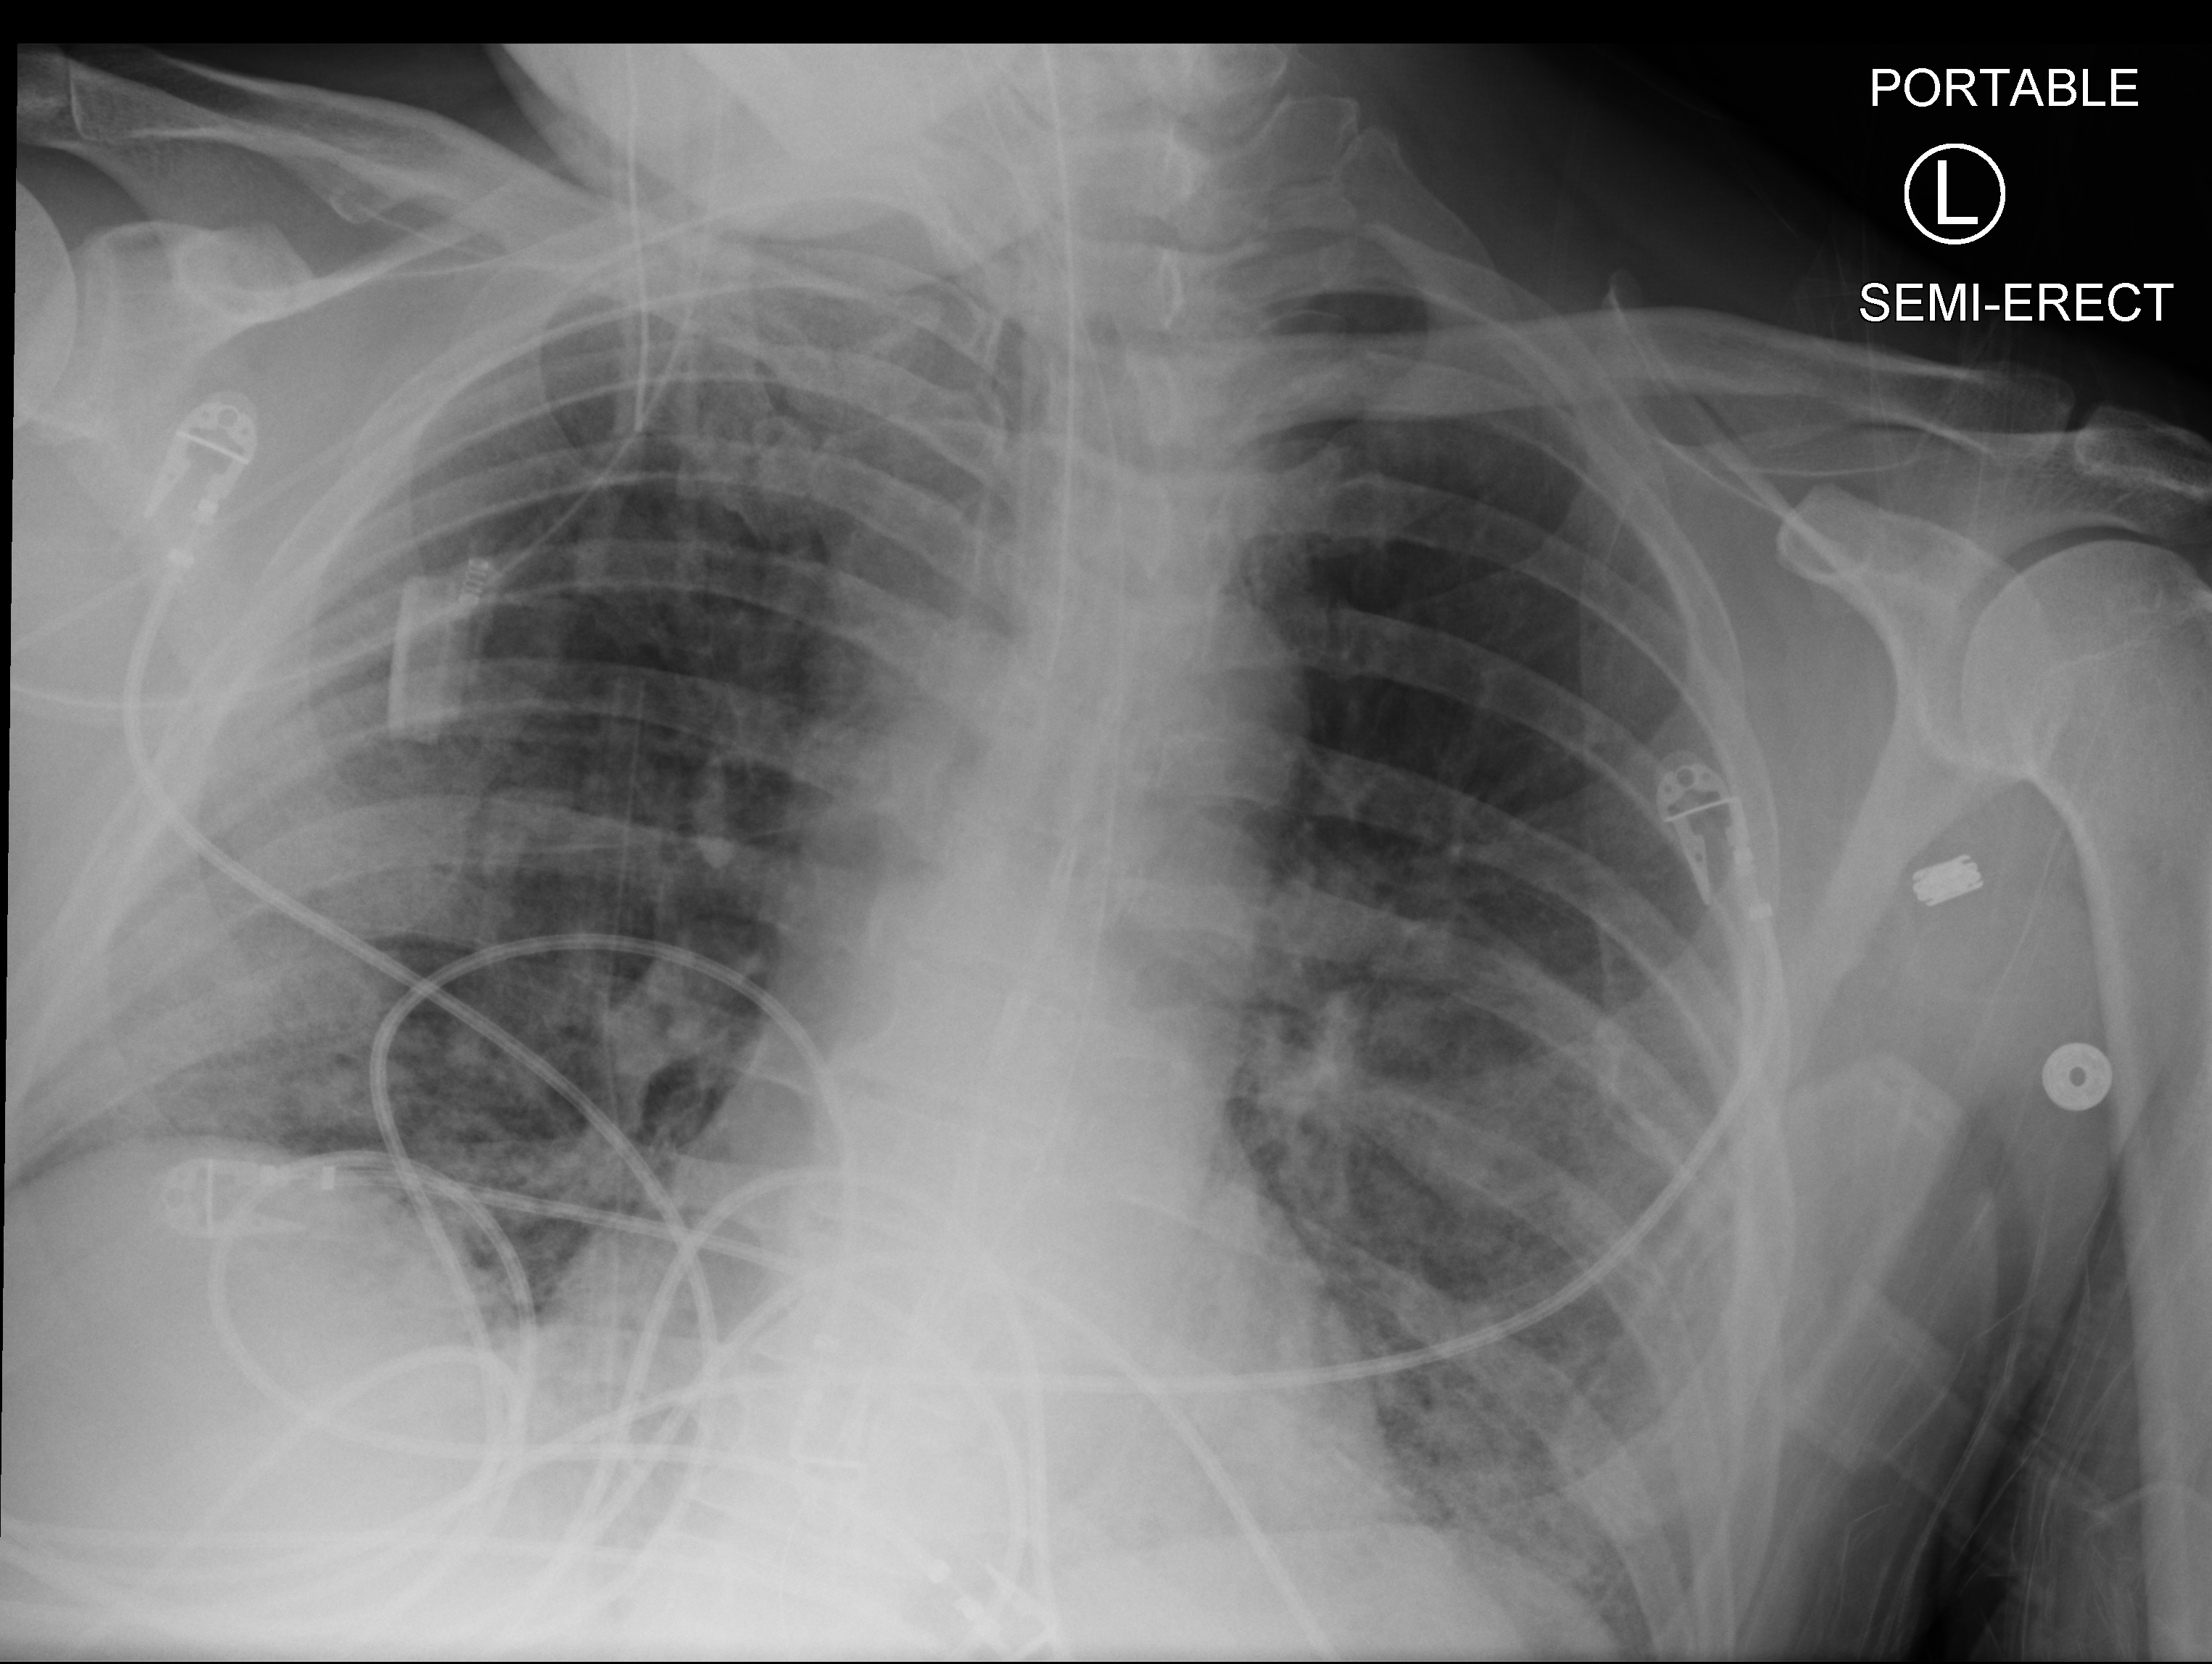
Bedside chest radiograph (computed radiography), anteroposterior (AP) projection. Male patient hospitalised with COVID-19, age 60–74 years.
From the hospital-stay record, not from the radiograph (when in the stay this image was taken is not recorded): mechanically ventilated during this hospital stay: yes; COPD (admission record): no.